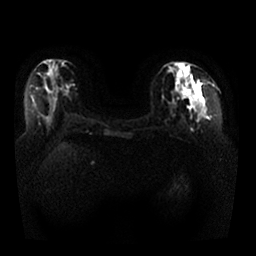
Breast MRI, one axial slice. Slice 12 of 25 in the series (ordered by position). Diffusion-weighted series; image 2 of 4 stored at this slice position (different b-values; order by instance number). 1.5 T. 4 mm slice thickness. 256 × 256 image matrix, field of view 350 × 350 mm. Female patient.
Annotated regions visible in this slice (outlined manually by an expert reader):
- tumour on diffusion-weighted imaging: box from (x=181, y=87) to (x=193, y=105) px